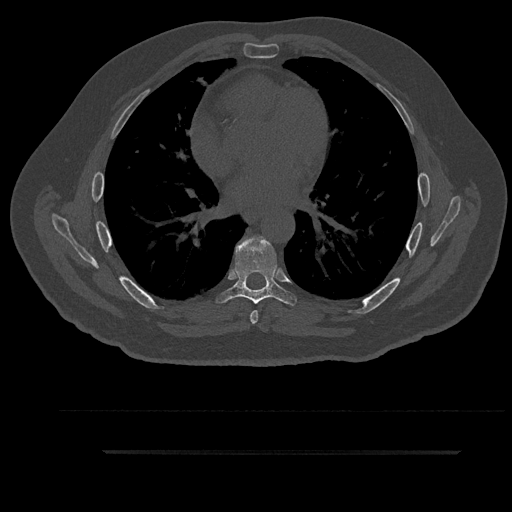
CT including the spine, one axial slice; slice 538 of 797 in the series (ordered by position); reconstruction kernel Br40s/3; bone window (W 1800 / L 400 HU); 0.5 mm slice thickness; 512 × 512 image matrix, field of view 432 × 432 mm. Male patient, age 63 years. From the clinical record (not read from this slice): primary cancer: renal; vertebrae with lytic lesions (as recorded): T8.
Outlined on this slice (semi-automatically segmented with operator editing):
- T6 vertebra: box from (x=249, y=236) to (x=261, y=324) px
- T7 vertebra: (x=216, y=236)–(x=297, y=306)